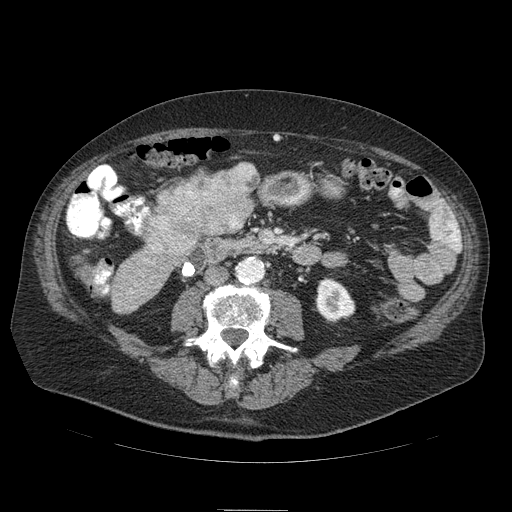
Contrast-enhanced abdominal CT (liver protocol), one axial slice. Position 14 of 103 along the scan axis. Reconstruction kernel STANDARD. 120 kVp. Soft-tissue window (W 400 / L 40 HU). 2.5 mm slice thickness. 512 × 512 image matrix, field of view 440 × 440 mm. Case-level facts recorded for this patient, not image findings: diagnosis: hepatocellular carcinoma (patient treated with transarterial chemoembolisation; whether this scan precedes or follows treatment is not stated here); TNM stage (as recorded): Stage-IIIA; Child-Pugh class: B; tumour differentiation: well differentiated; tumour nodularity: multinodular.
Outlined on this slice (semi-automatically segmented with operator editing):
- mass: bounding box [x1, y1, x2, y2] px = [148, 161, 256, 258]